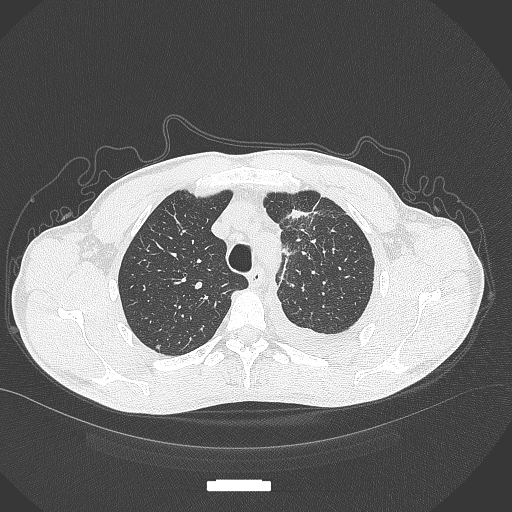
Chest CT, one axial slice; position 272 of 371 along the scan axis; 120 kVp; lung window (W 1500 / L -600 HU); 512 × 512 image matrix. Patient: male, 49 years. Case-level facts recorded for this patient, not image findings: clinical TNM (as recorded): T1c N1 M1.
Structures marked on this image (bounding box drawn by a radiologist):
- lung tumour (recorded histology: adenocarcinoma): bounding box [x1, y1, x2, y2] px = [280, 207, 316, 225]